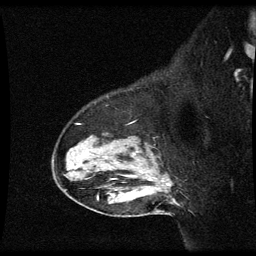
Breast MRI (dynamic contrast-enhanced), one sagittal slice; slice 45 of 60 in the series (ordered by position); dynamic contrast-enhanced series, image 2 of 3 at this slice position (ordered by acquisition); 1.5 T; TE 4.2 ms, TR 8.9 ms; 2 mm slice thickness; 256 × 256 image matrix, field of view 200 × 200 mm. Female patient, age 49 years. Case-level facts recorded for this patient, not image findings: setting: breast cancer imaged before/during neoadjuvant chemotherapy; receptor status: HR-positive, HER2-negative.
Structures marked on this image (semi-automatic segmentation, software-assisted and operator-edited):
- analysis volume of interest (the breast-tissue region the enhancement analysis was run in; not a lesion): bounding box (x1, y1, x2, y2) in pixels: (53, 134, 177, 205)
- tumour enhancement mask (voxels above the 70 % enhancement threshold inside the analysis volume of interest): (168, 184, 170, 187)